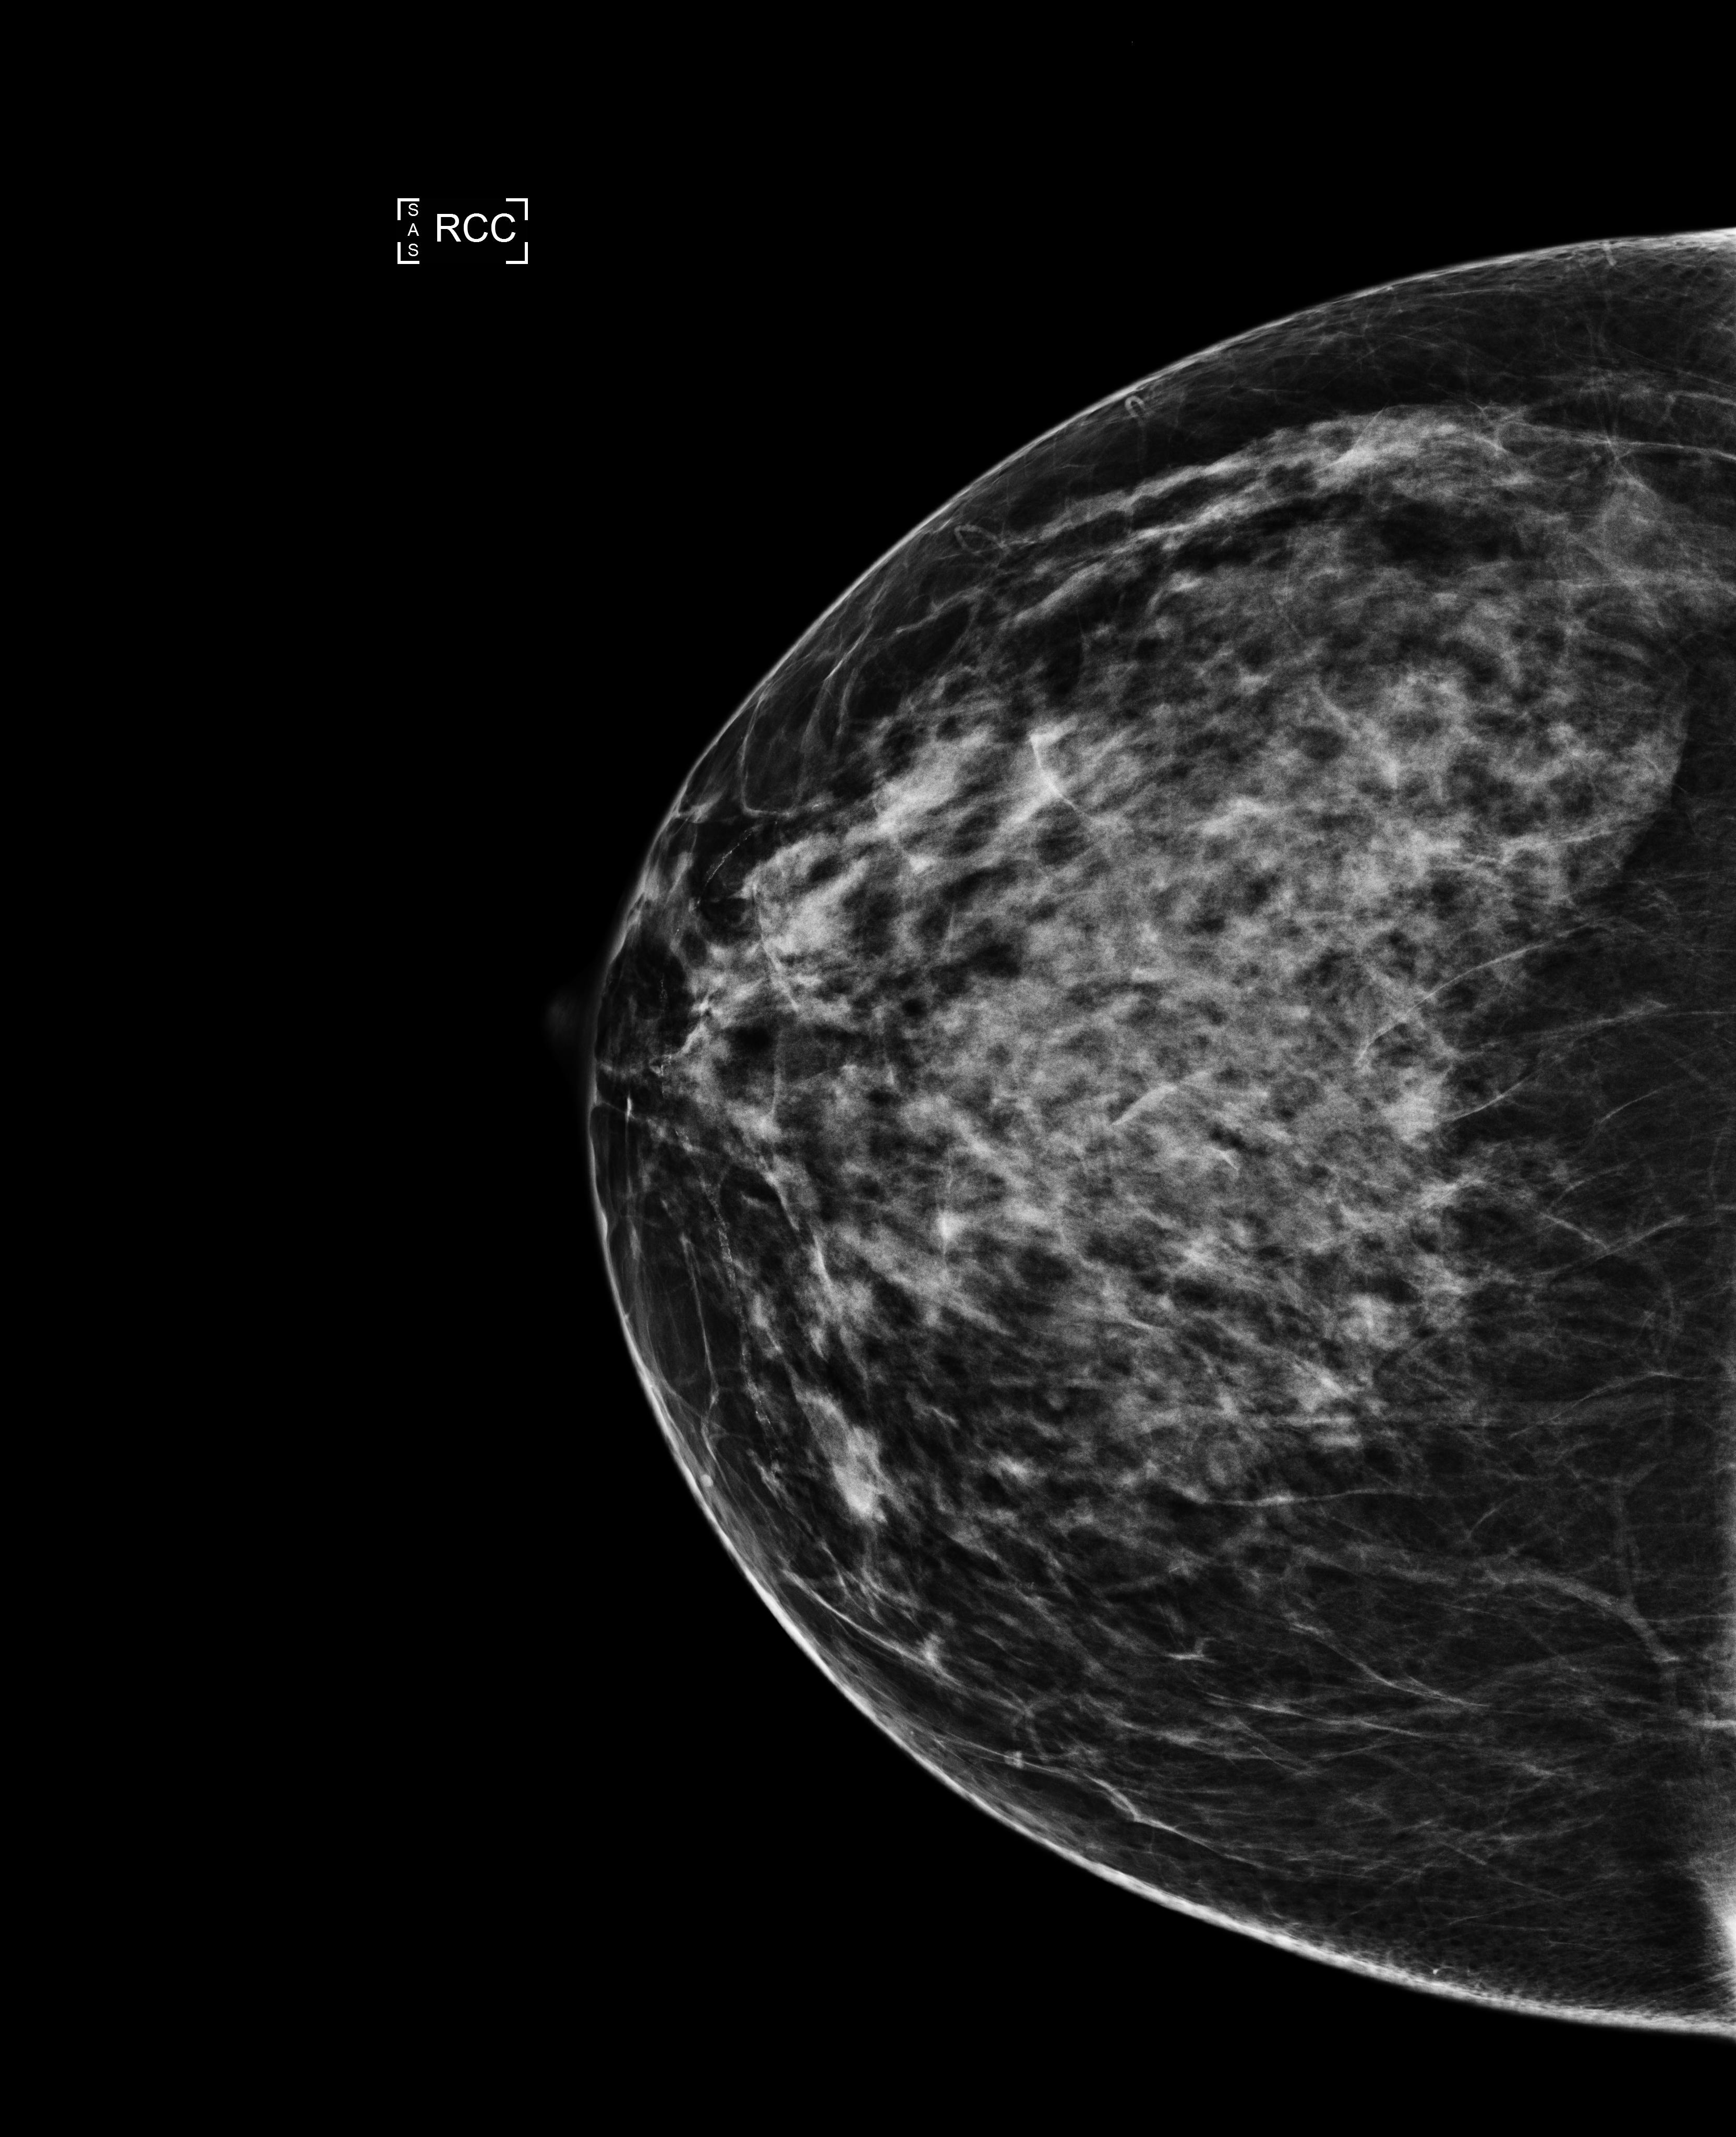
Full-field digital mammogram (FFDM), right breast, craniocaudal (CC) view, annual screening mammography examination, compressed breast thickness 68 mm. Patient: female, 44 years.
BI-RADS breast density category at the screening exam (both breasts, scale 1–4): 3. Final BI-RADS assessment for this screening round (tomosynthesis exam, both breasts): category 1. Recall: no recall after this screen.